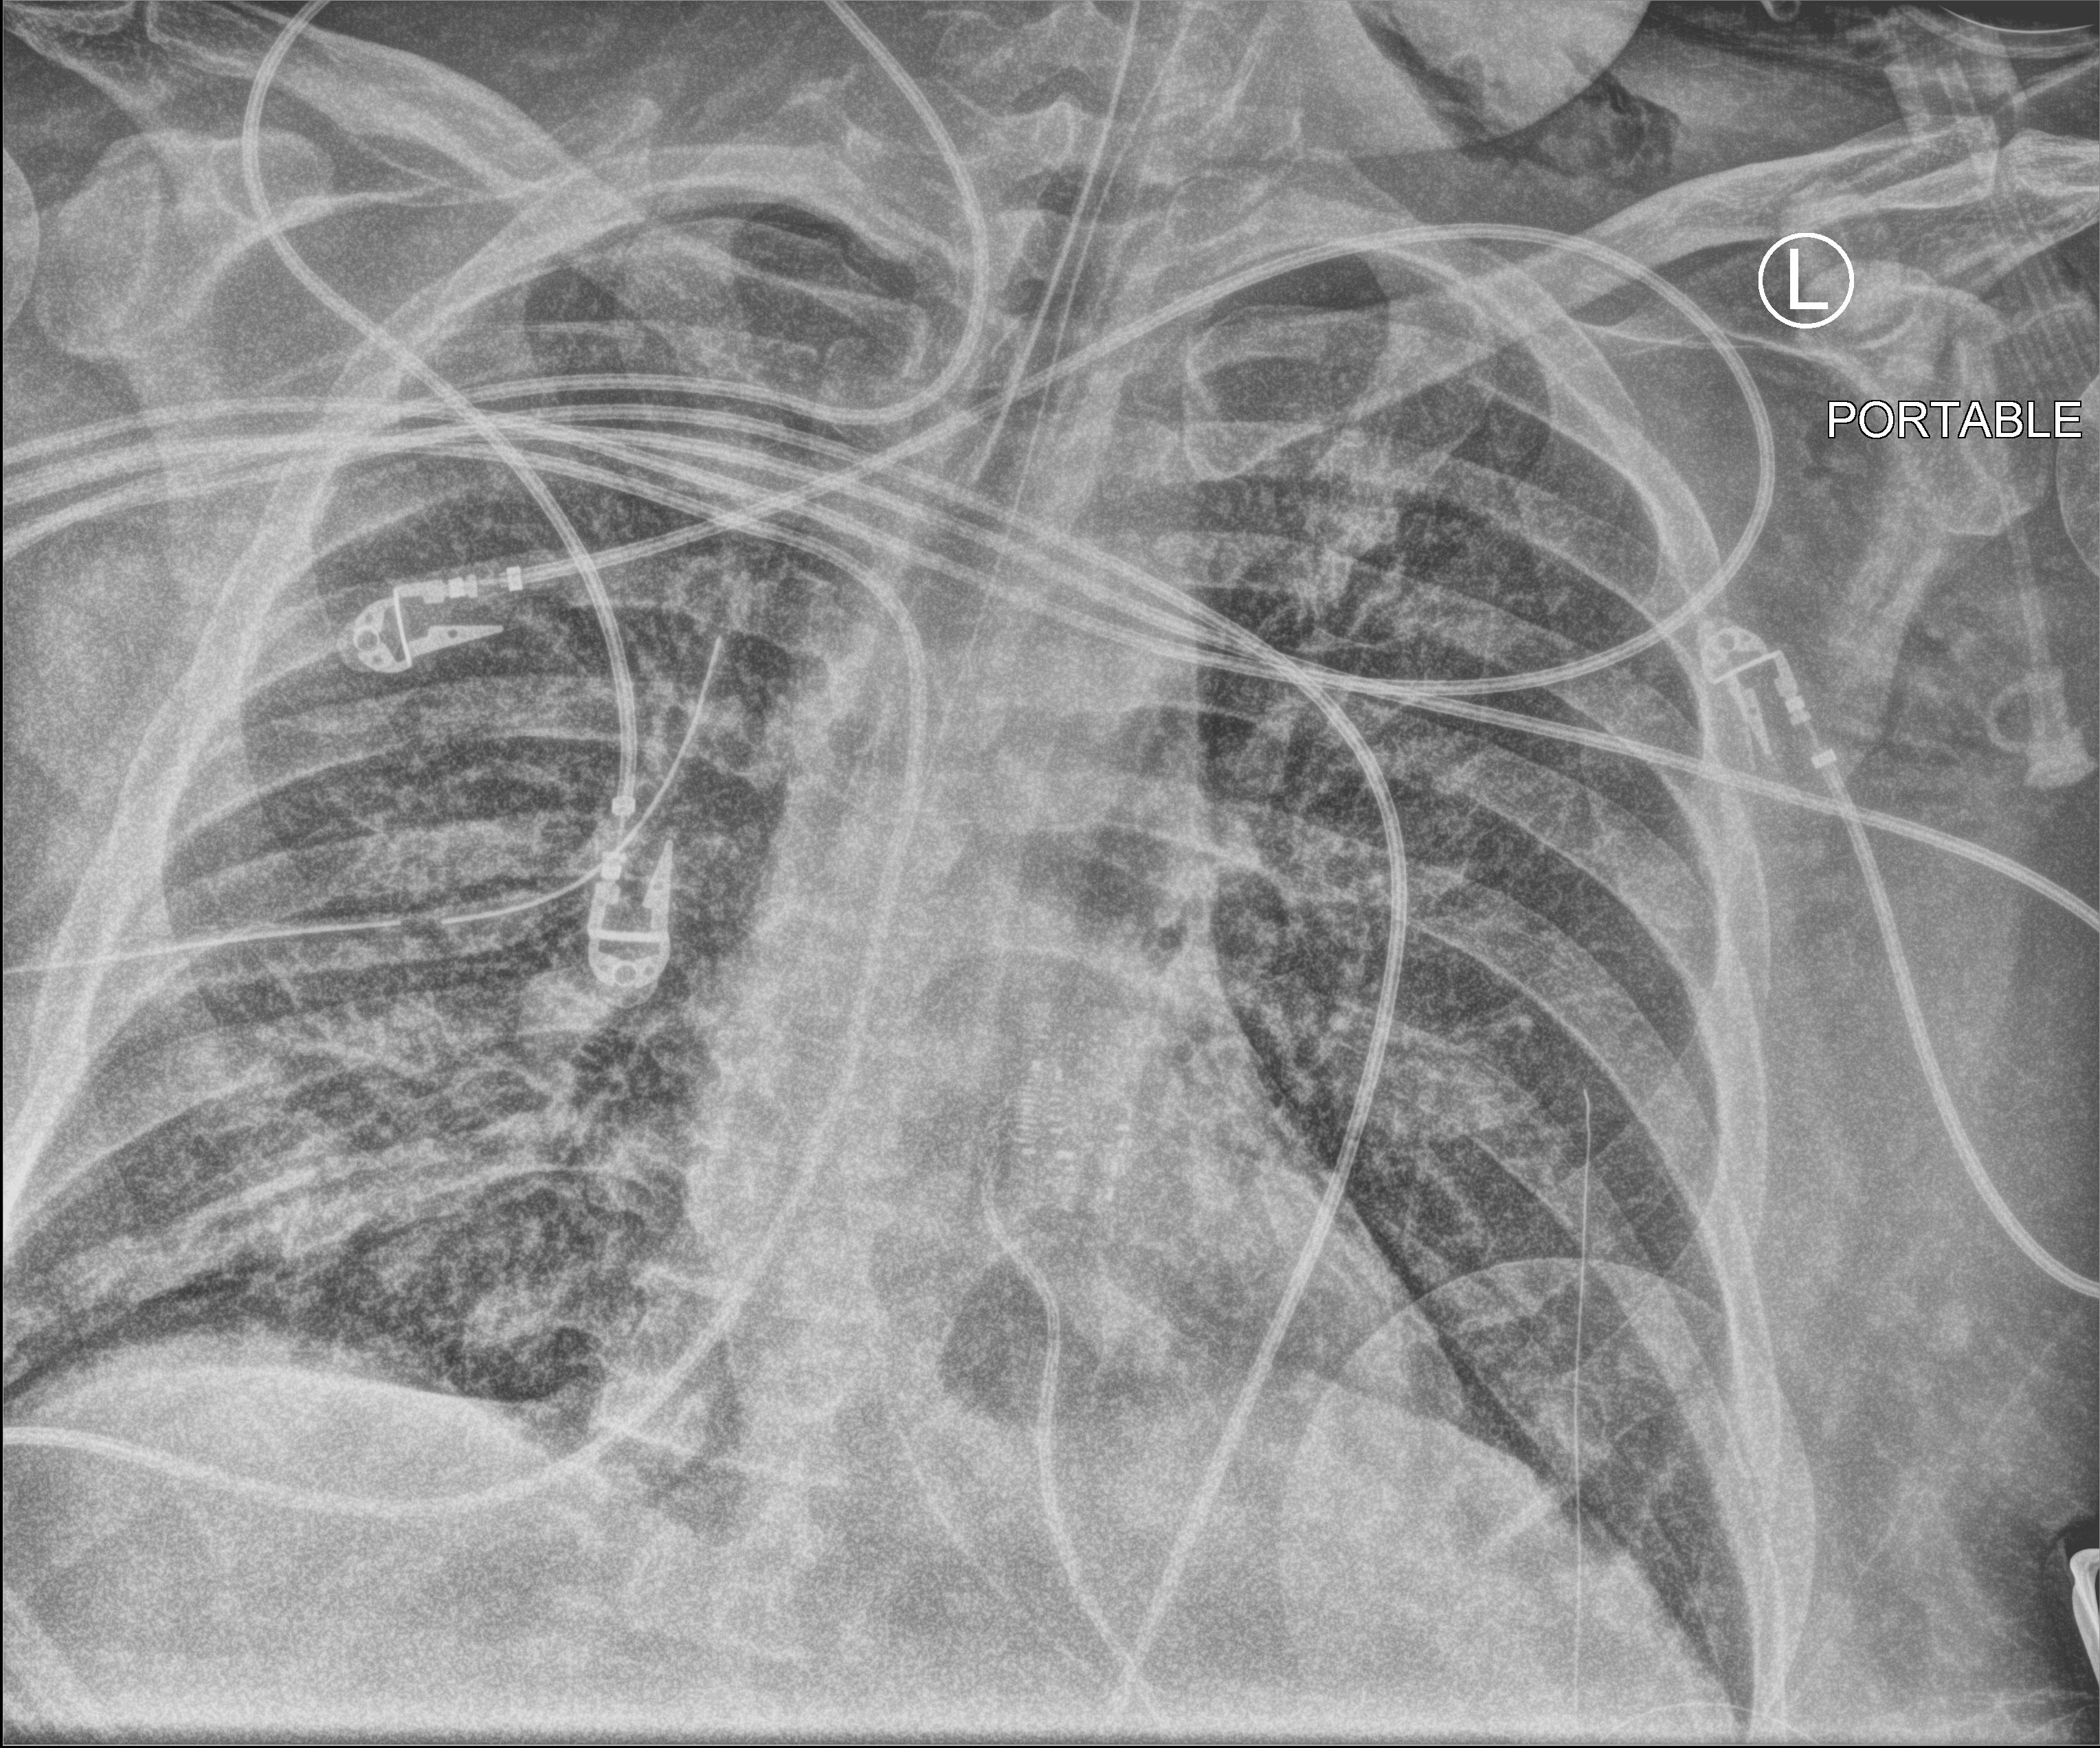
Bedside chest radiograph (computed radiography), anteroposterior (AP) projection. Adult patient hospitalised with COVID-19, age 18–59 years.
Admission-level facts for this patient (not findings on this image; timing relative to this image not recorded): admitted to intensive care during this hospital stay: yes.